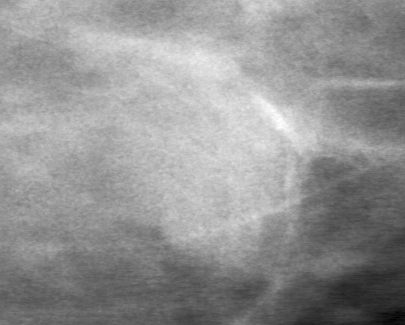
Cropped region of a digitized screen-film mammogram centred on a radiologist-marked abnormality; left breast; MLO view; BI-RADS breast density category 3 (scale 1–4).
- Mass, shape oval, margins obscured; BI-RADS assessment category 0 (incomplete: needs additional imaging); subtlety rating 4 on a 1 (subtle) to 5 (obvious) scale; pathology (as recorded): benign.